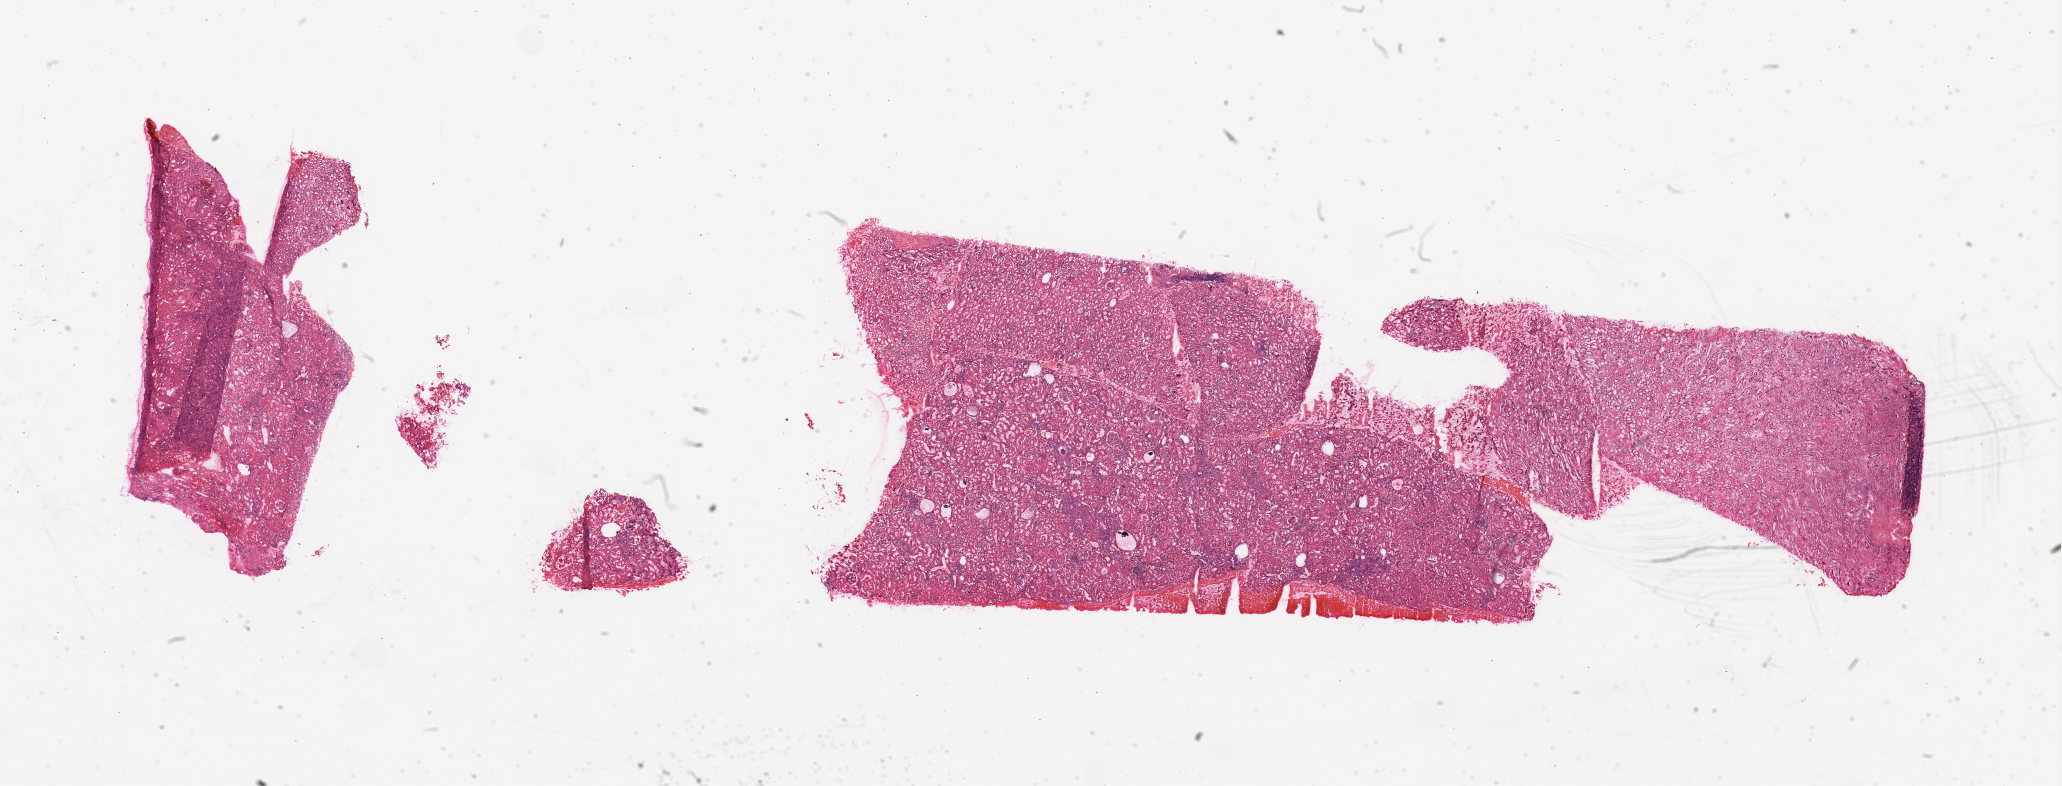
Hematoxylin and eosin (H&E) stained whole-slide image — low-resolution overview of the scanned area, about 33.1 x 12.6 mm (from a 20x scan), frozen section from the top of the tissue portion, solid tissue normal (non-tumour tissue) sample from the kidney. Patient: male, age at initial diagnosis 64 years.
This section: solid tissue normal sample (biorepository sample class). Patient diagnosis: Clear cell adenocarcinoma, NOS.